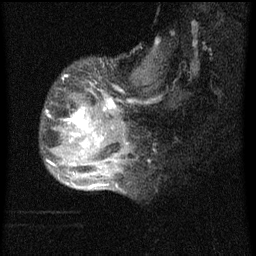
Breast MRI (dynamic contrast-enhanced), one sagittal slice. Slice 20 of 60 in the series (ordered by position). Dynamic contrast-enhanced series, image 2 of 4 at this slice position (ordered by acquisition). 1.5 T. TE 4.2 ms, TR 8 ms. 2 mm slice thickness. 256 × 256 image matrix. Female patient, age 50 years.
Annotated regions visible in this slice (semi-automatically segmented with operator editing):
- analysis volume of interest (the breast-tissue region the enhancement analysis was run in; not a lesion): bounding box <43,62,124,177> (left, top, right, bottom; pixels)
- tumour enhancement mask (voxels above the 70 % enhancement threshold inside the analysis volume of interest): <54,100,116,177>